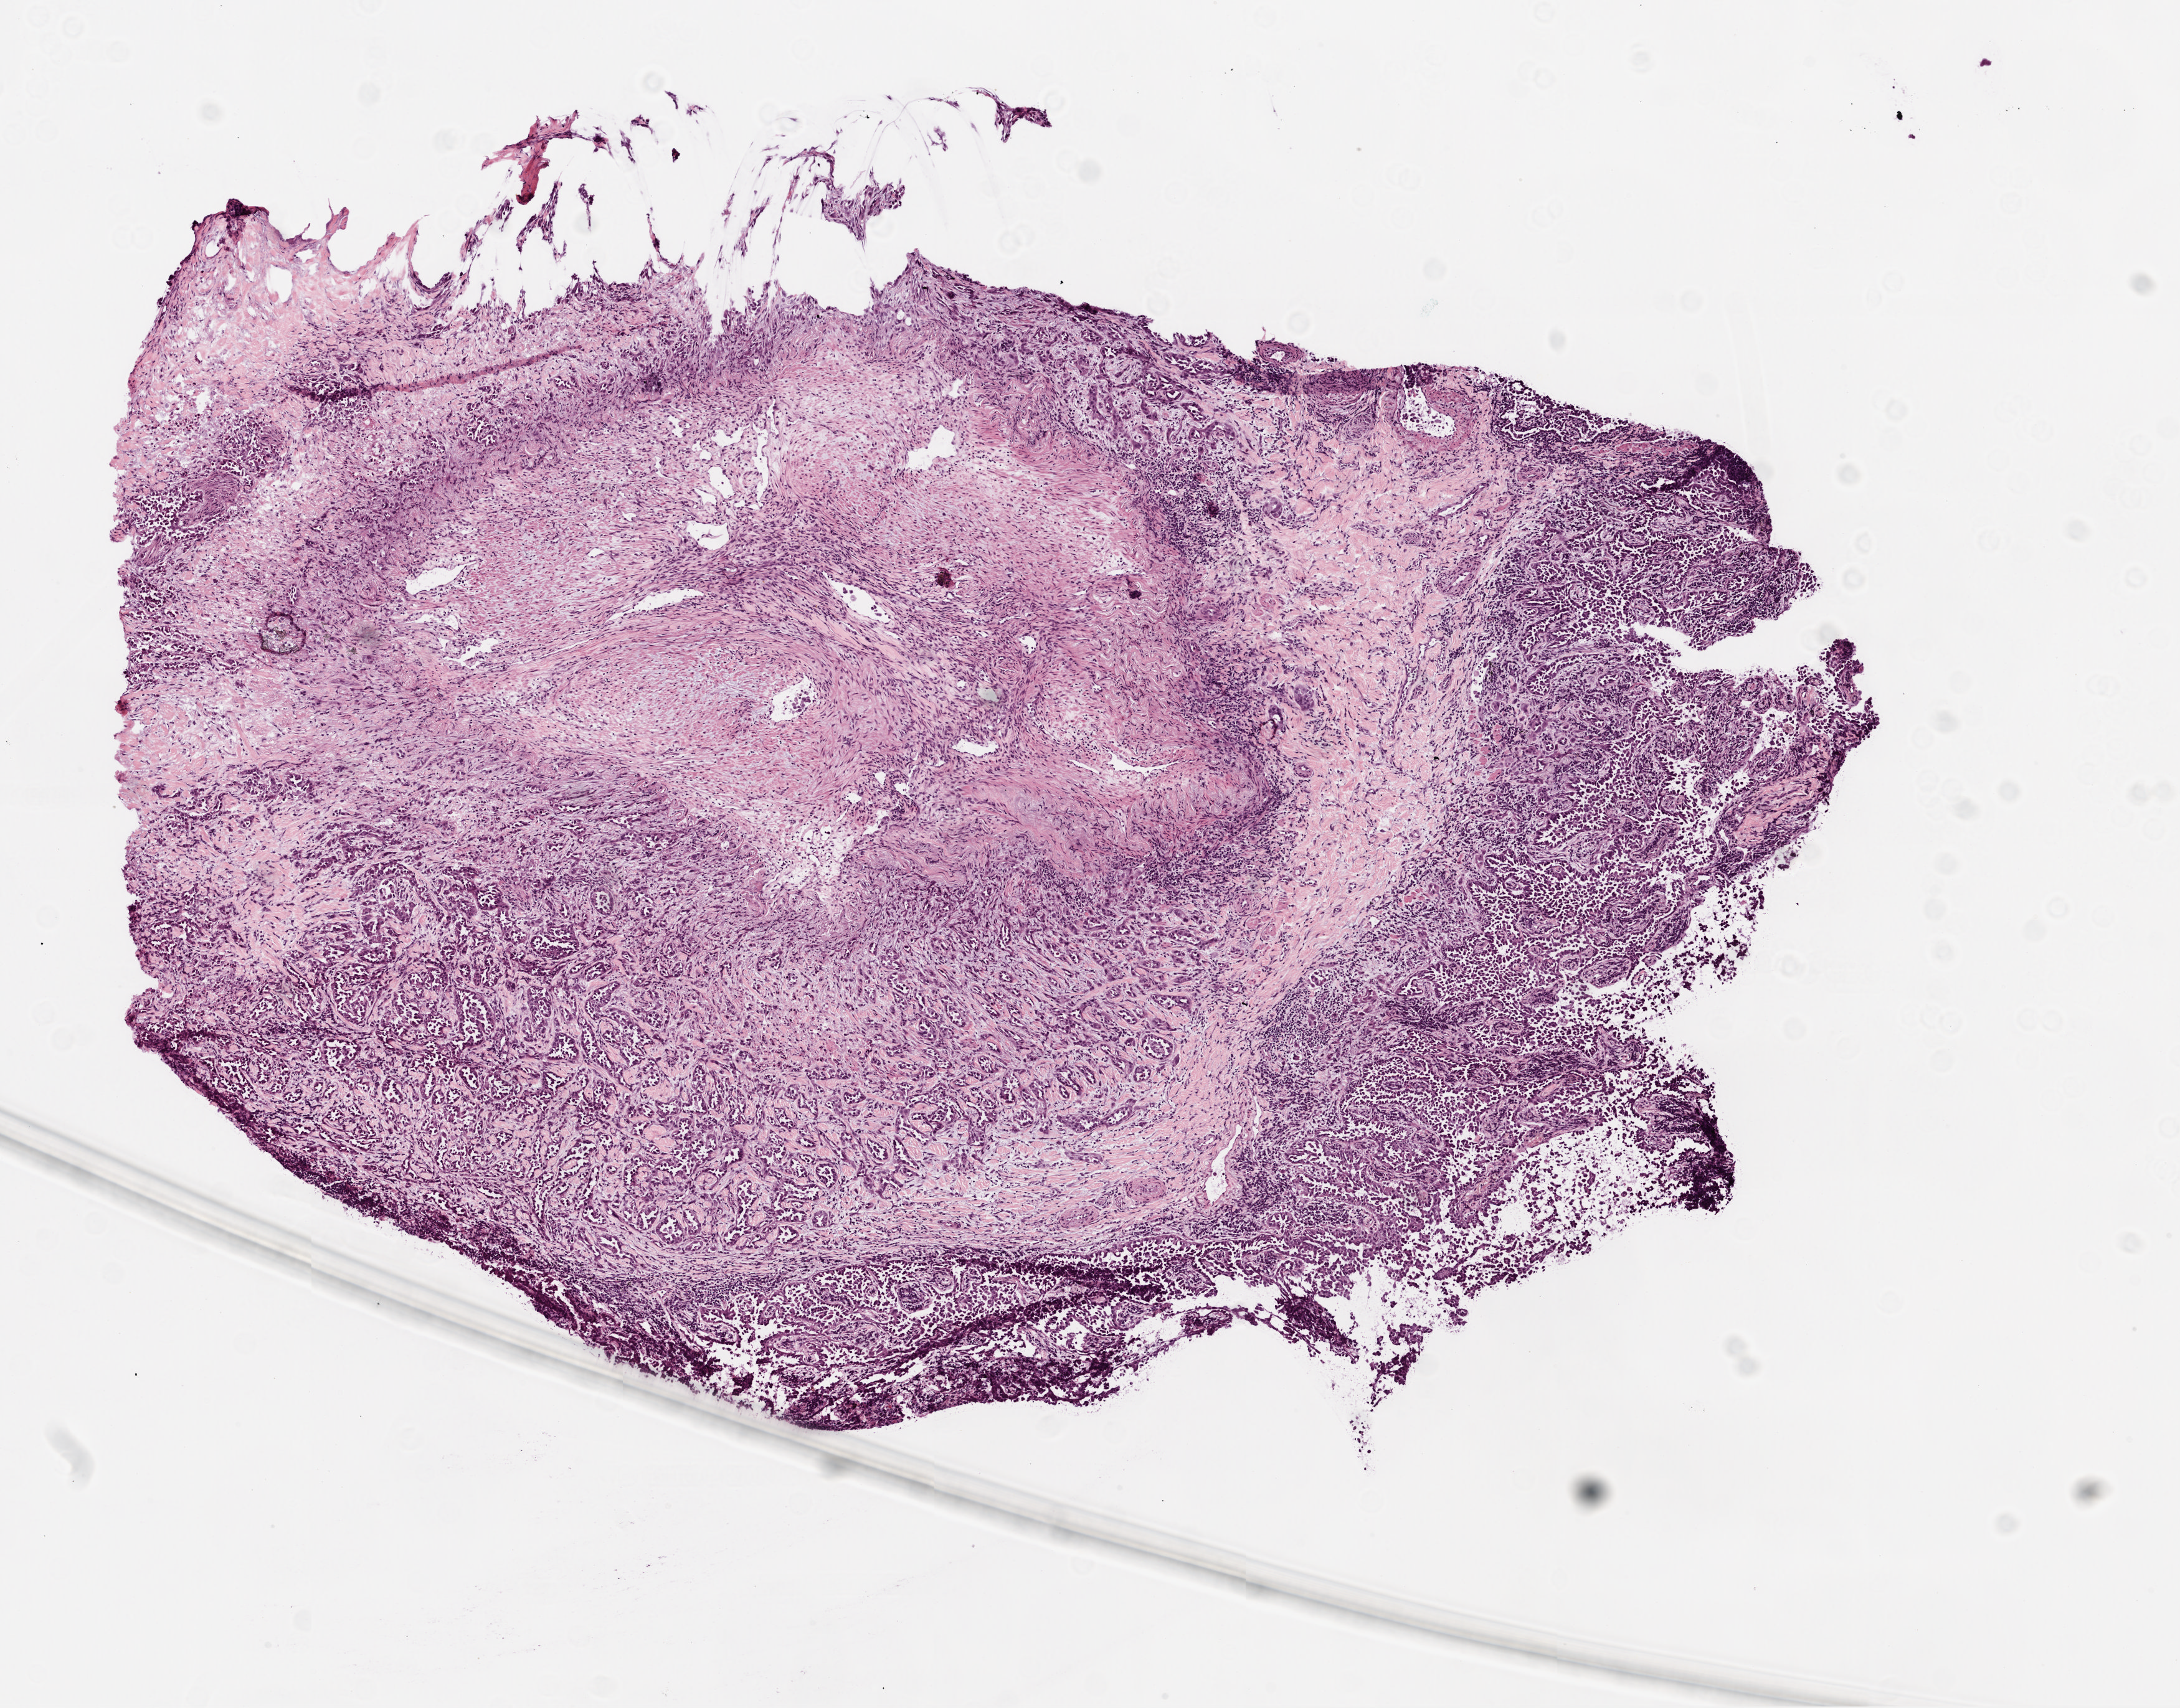
H&E-stained whole-slide image — low-resolution overview of the scanned area, about 7.0 x 5.5 mm (slide scanned at 20x), frozen section, lung, primary tumour sample. Female patient; age at initial diagnosis 66 years. Slide review estimates, as recorded: tumour cells 95%, tumour nuclei 80%, normal cells 0%, stromal cells 0%, necrosis 5%.
- AJCC pathologic stage: IIB
- laterality: left
- diagnosis: Invasive micropapillary carcinoma (upper lobe, lung)